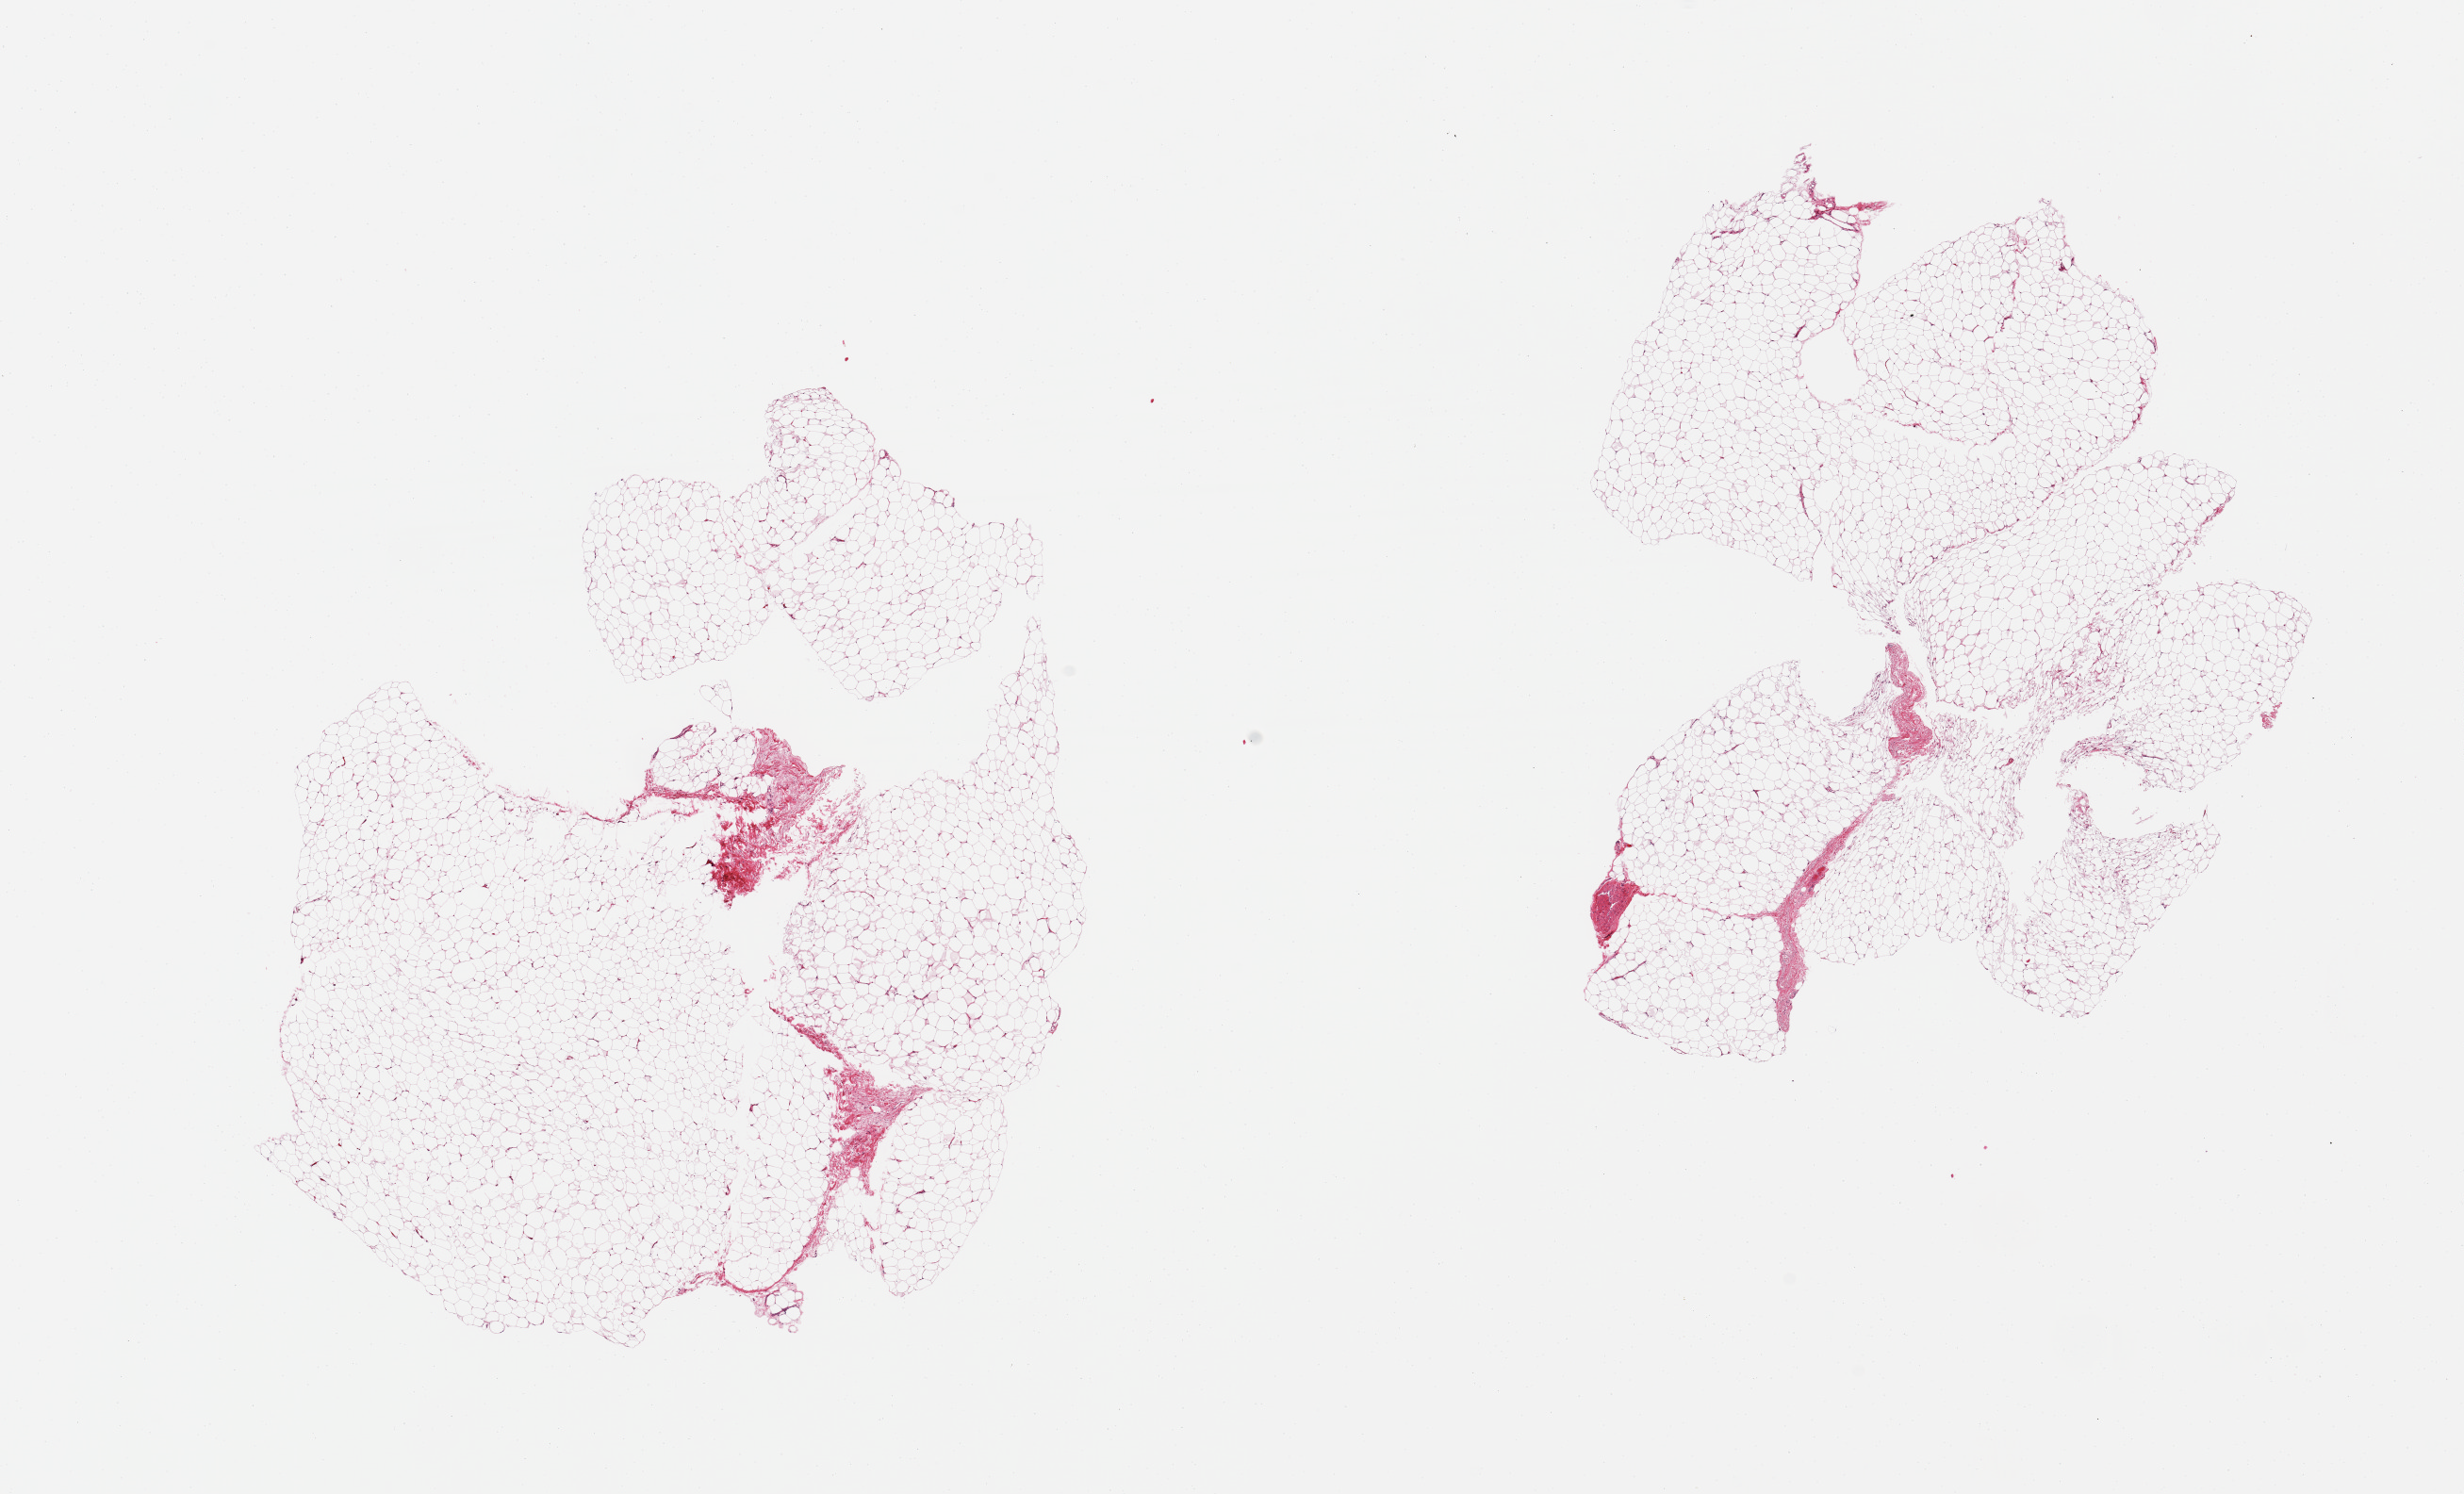
Whole-slide image, hematoxylin and eosin (H&E) stain, shown as a low-resolution overview of the whole scanned area (about 20.7 x 12.5 mm, acquisition: 20x scan), PAXgene-fixed, paraffin-embedded tissue, section of adipose tissue (target tissue), tissue donor sample.
Reviewer comment on this tissue sample: 2 pieces; <5% fibrous content.